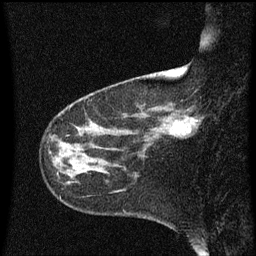
Breast MRI (dynamic contrast-enhanced), one sagittal slice. Slice 18 of 60 in the series (ordered by position). Dynamic contrast-enhanced series, image 2 of 3 at this slice position (ordered by acquisition). 1.5 T. TE 4.2 ms, TR 8.4 ms. 2 mm slice thickness. 256 × 256 image matrix, field of view 200 × 200 mm. Patient: female, 41 years. From the clinical record (not read from this slice): setting: breast cancer imaged before/during neoadjuvant chemotherapy; receptor status: triple-negative.
Outlined on this slice (semi-automatic segmentation, software-assisted and operator-edited):
- analysis volume of interest (the breast-tissue region the enhancement analysis was run in; not a lesion): bounding box [x1, y1, x2, y2] px = [158, 102, 203, 141]
- tumour enhancement mask (voxels above the 70 % enhancement threshold inside the analysis volume of interest): [189, 120, 199, 133]